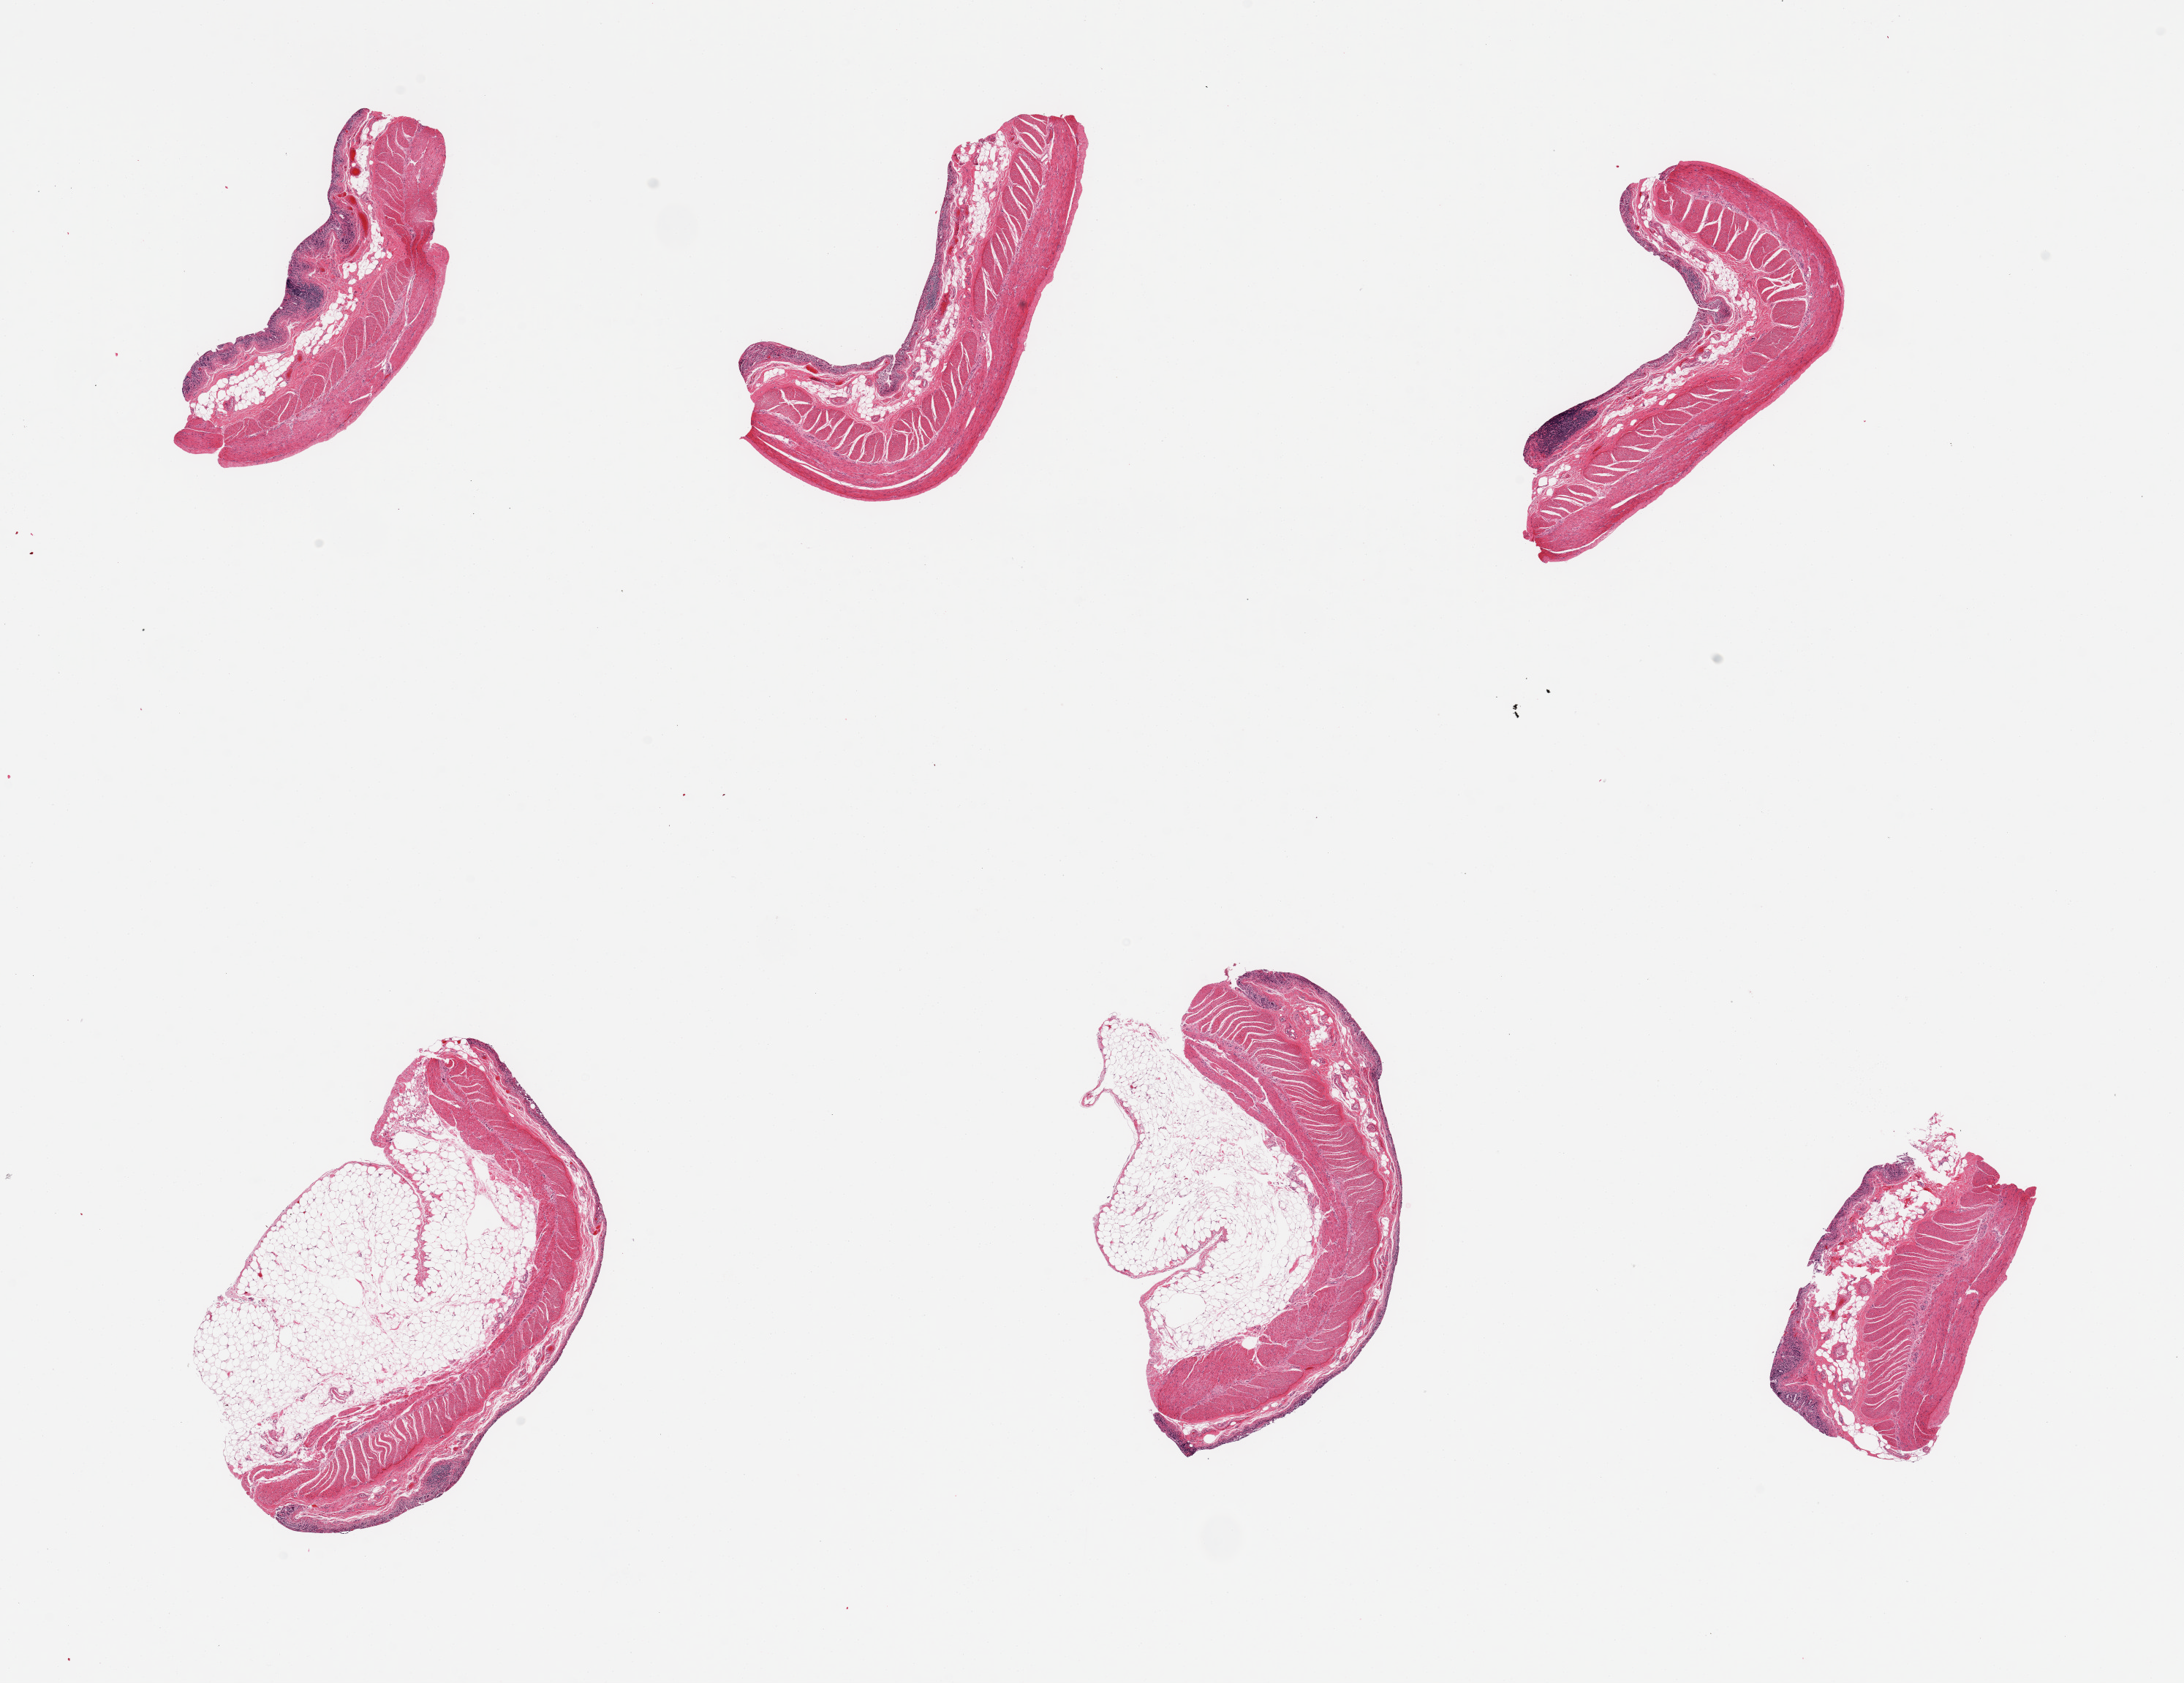
Whole-slide image, H&E stain, shown as a low-resolution overview of the whole scanned area (about 23.6 x 18.2 mm, from a 20x scan); PAXgene-fixed, paraffin-embedded tissue; sampled site (target tissue): ileum; donor tissue sample. Male donor.
Reviewer comment on this tissue sample: 6 pieces, muscularis, sloughed mucosa. Insufficient target lymphoid aggregates.